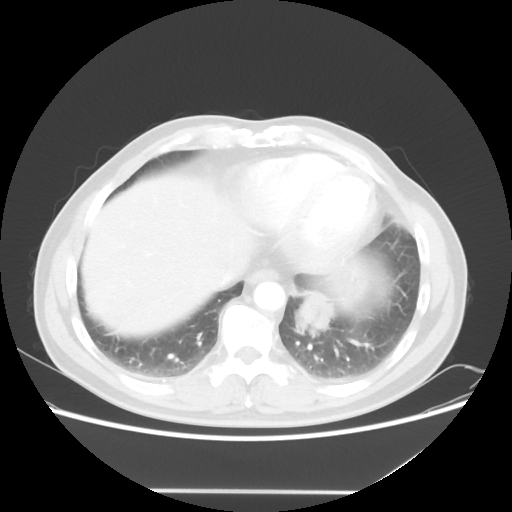
Chest CT, one axial slice; position 16 of 56 along the scan axis; 120 kVp; lung window (W 1500 / L -600 HU); 5 mm slice thickness; 512 × 512 image matrix, field of view 385 × 385 mm. Patient: male, 61 years. From the clinical record (not read from this slice): clinical TNM (as recorded): T1c N0 M0; histopathological grade: G3.
Outlined on this slice (rectangle marked by the reading radiologist):
- lung tumour (recorded histology: adenocarcinoma): bounding box [x1, y1, x2, y2] px = [287, 286, 337, 340]